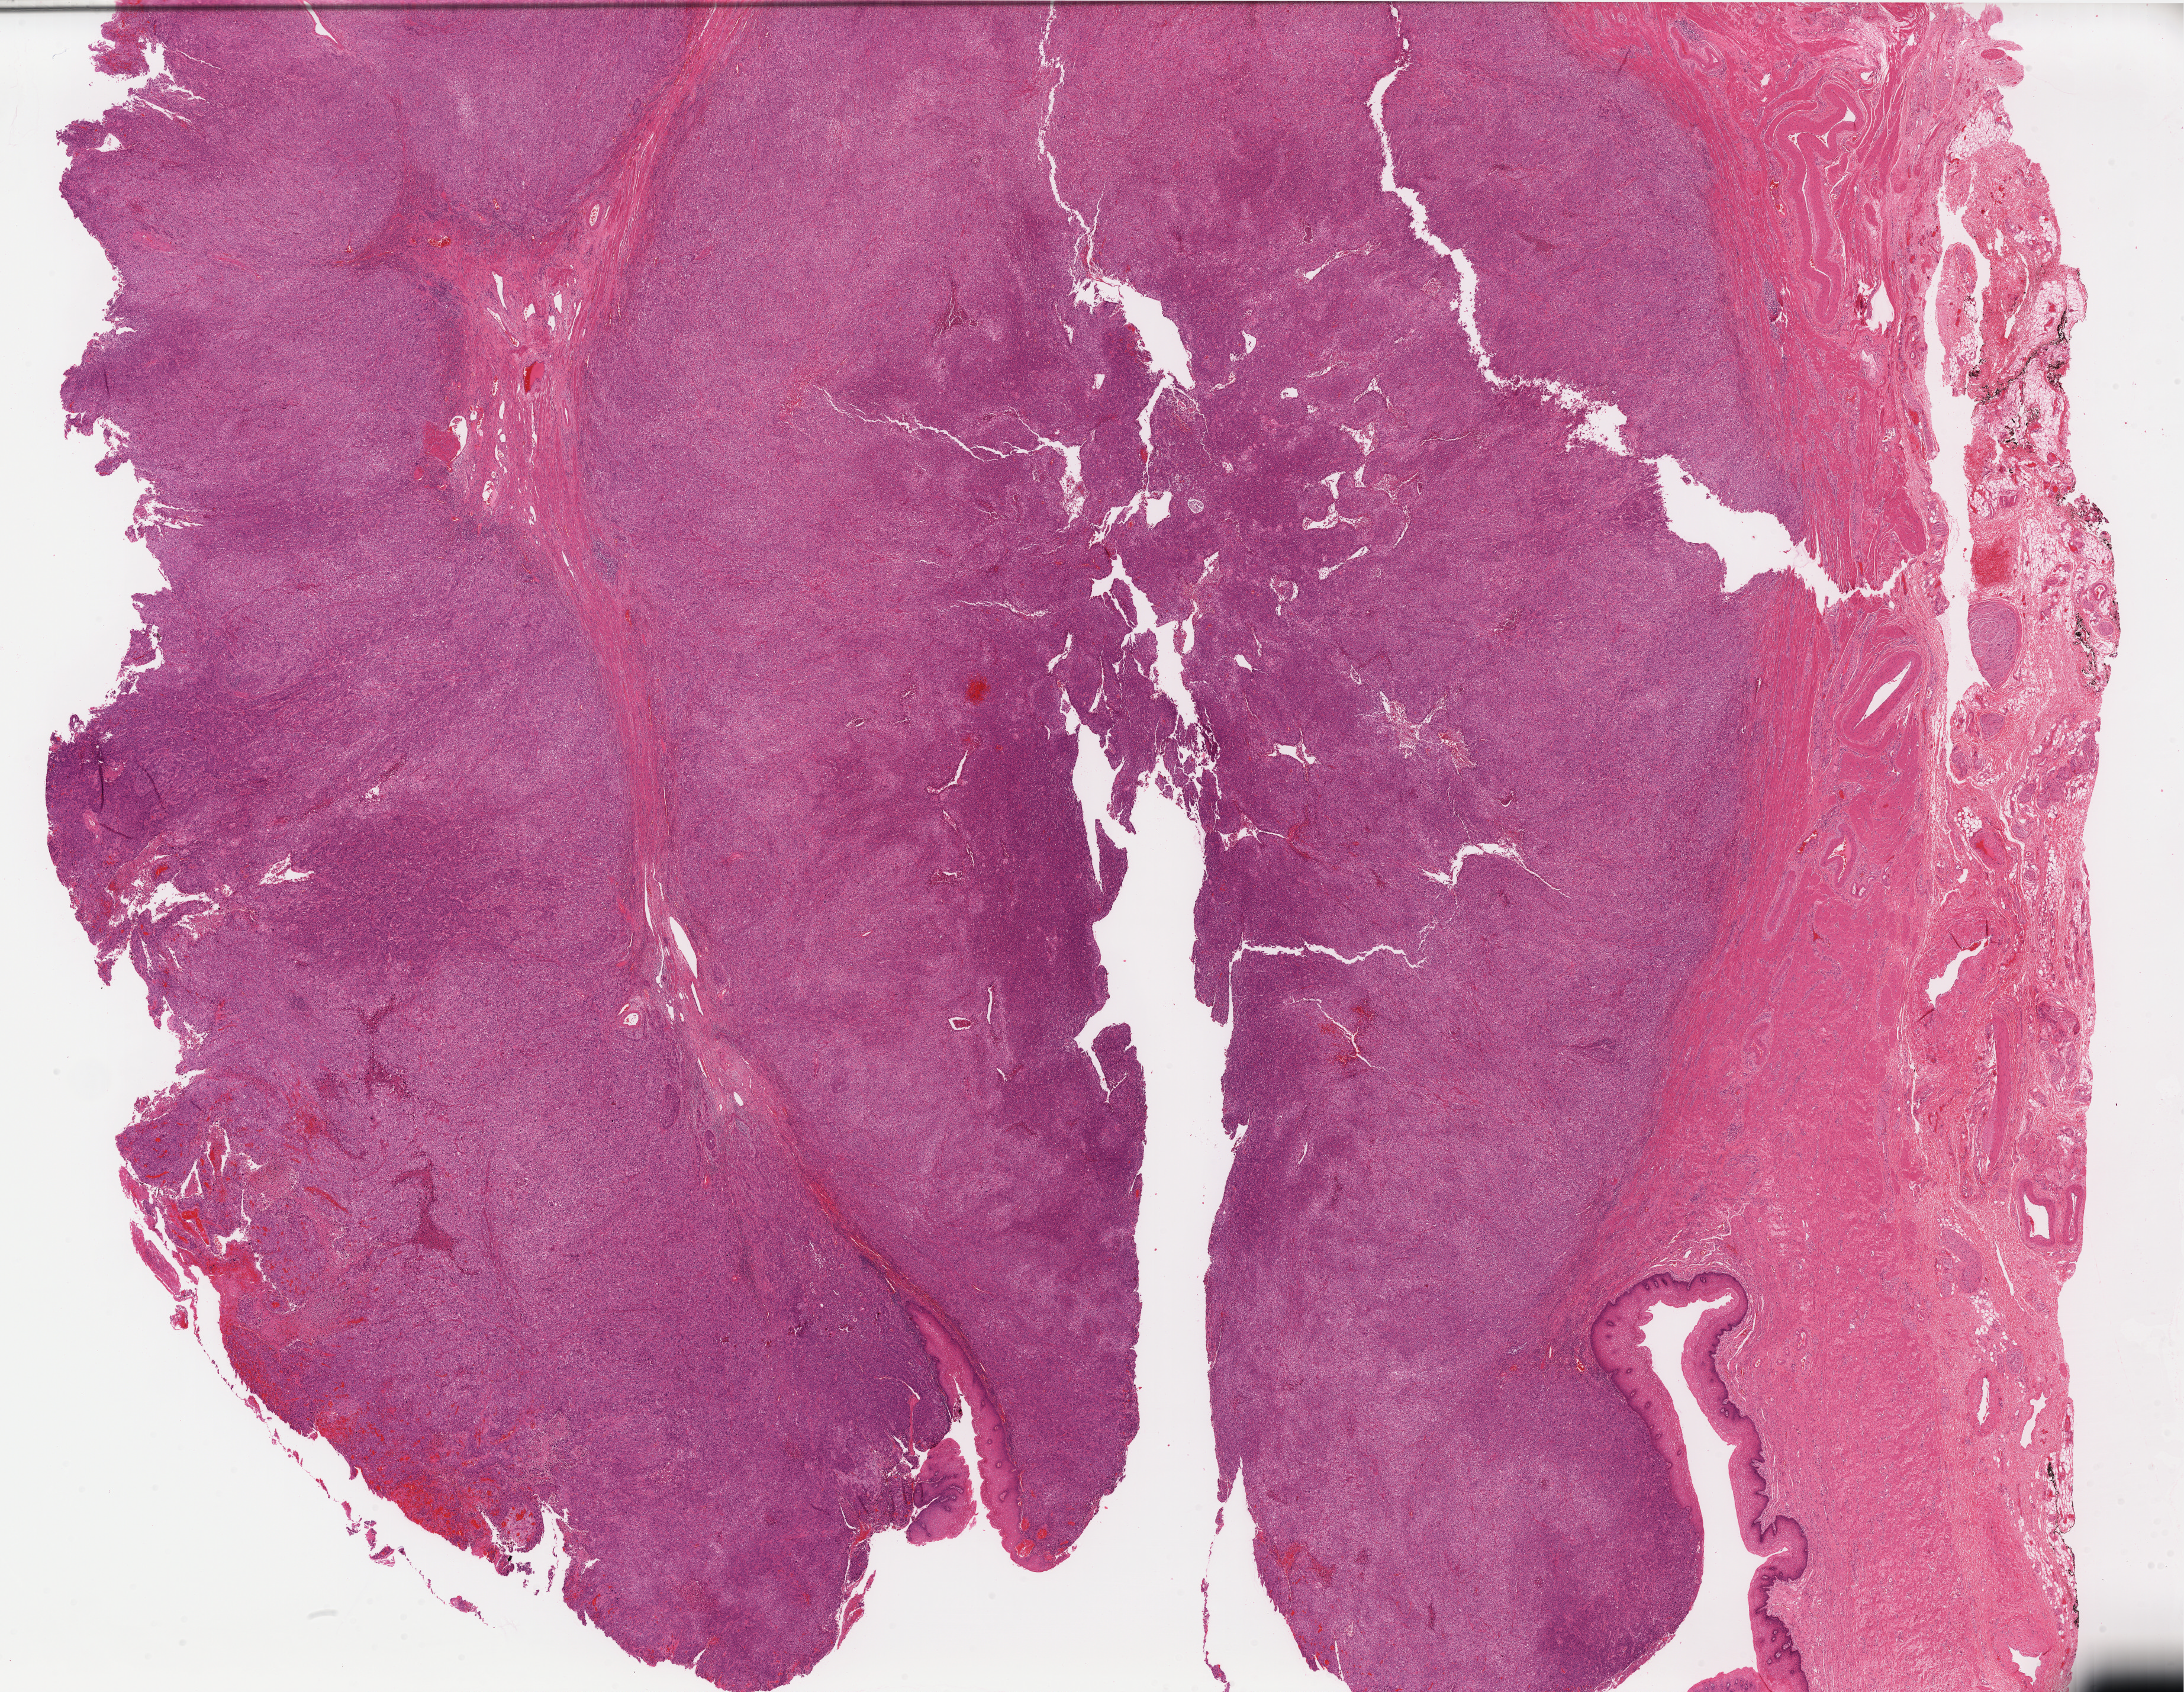
Digitized H&E-stained tissue section (whole slide), whole scanned area (about 29.5 x 22.9 mm) shown as a low-resolution overview, FFPE section, primary tumour sample from the cervix. Patient: female, age at initial diagnosis 21 years. Histologic grade: G3 (poorly differentiated).
- pathologic diagnosis: Squamous cell carcinoma, keratinizing, NOS (cervix uteri)
- FIGO stage: IB2